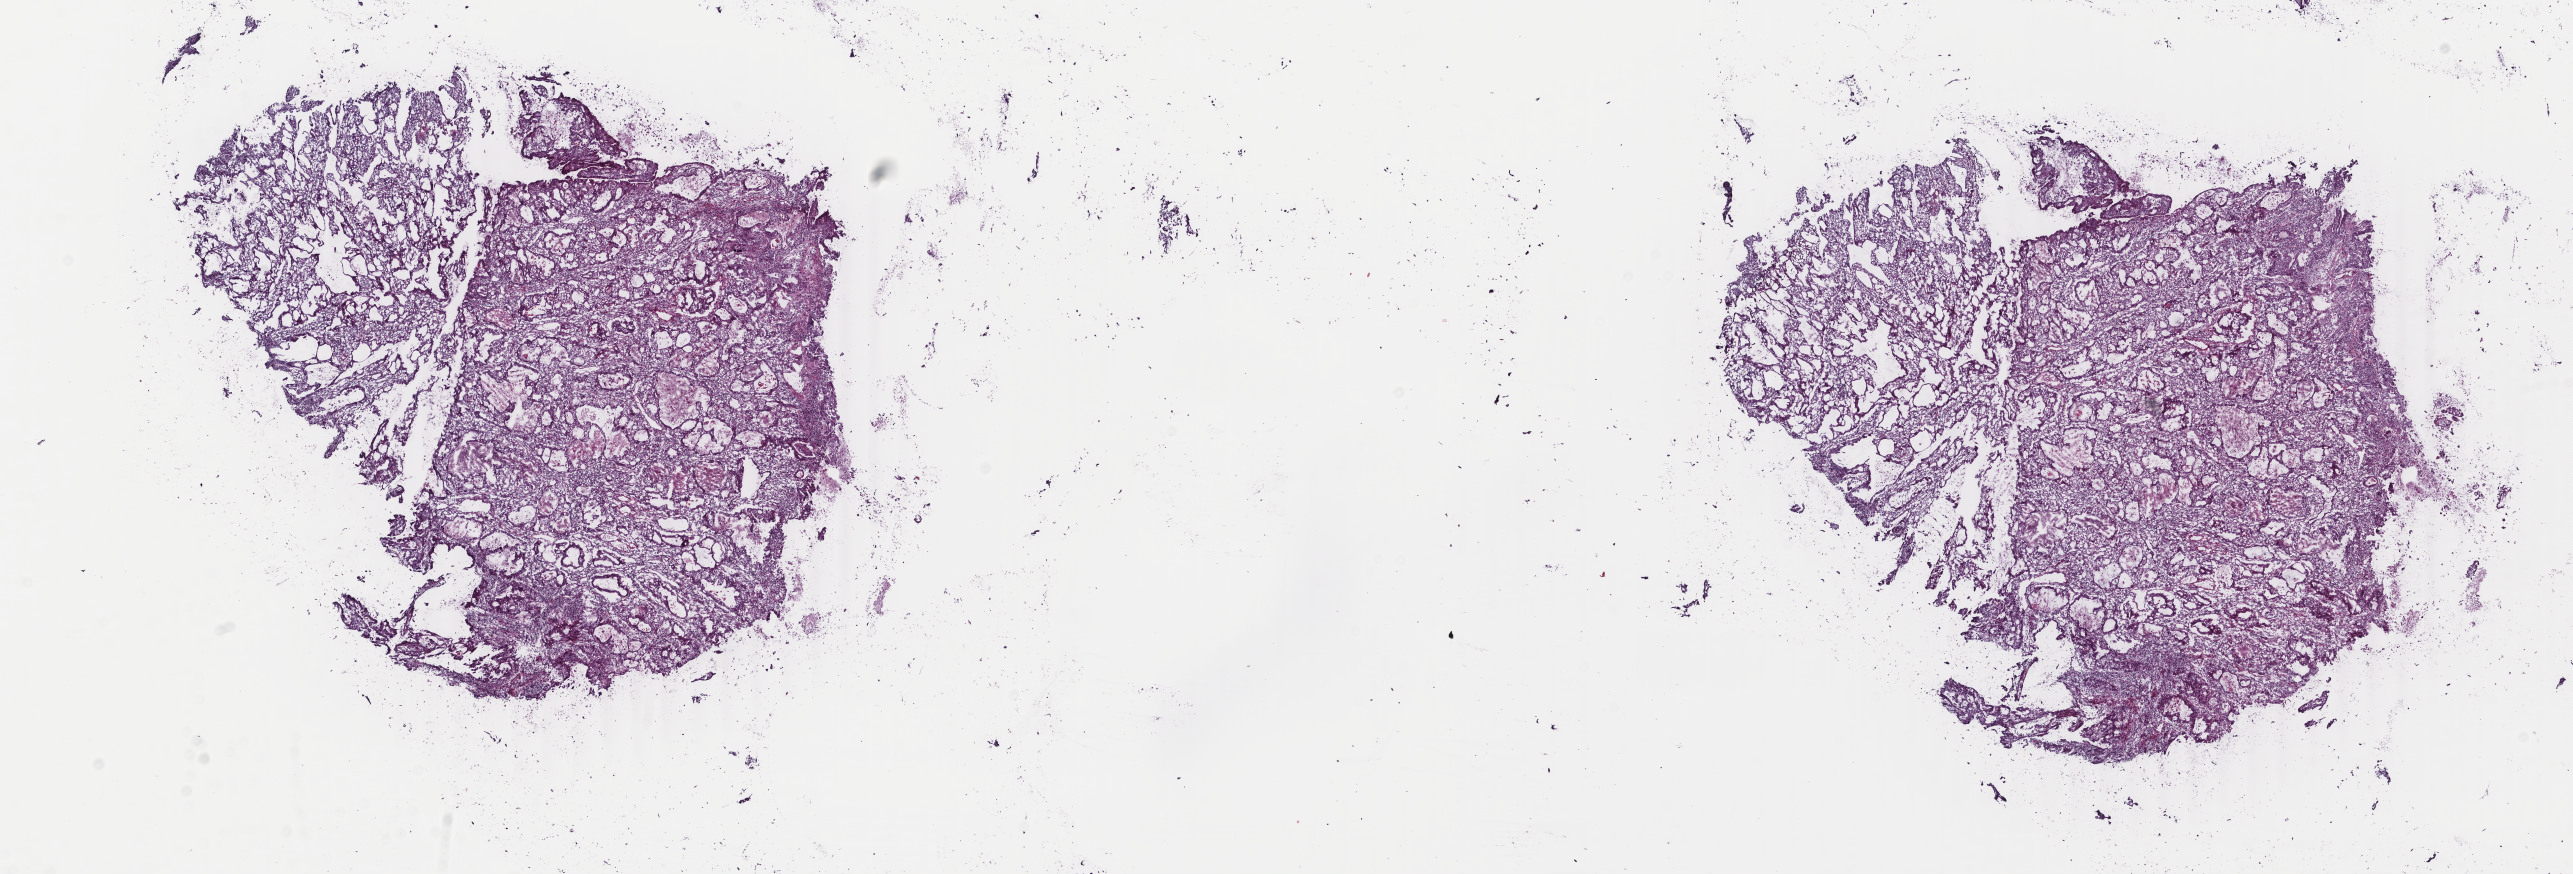
H&E whole-slide image — a low-resolution overview of the entire scanned area, about 20.5 x 7.0 mm (acquisition: 40x scan). Frozen section from the top of the tissue portion. Uterus, primary tumour sample. Female patient; age at initial diagnosis 31 years. Histologic grade: G2 (moderately differentiated). Slide review estimates, as recorded: tumour cells 80%, tumour nuclei 80%, normal cells 0%, stromal cells 10%, necrosis 10%. Infiltration values recorded for this section: lymphocyte infiltration 40%, monocyte infiltration 20%, neutrophil infiltration 20%.
FIGO stage: IA. Pathologic diagnosis: Endometrioid adenocarcinoma, NOS (endometrium).